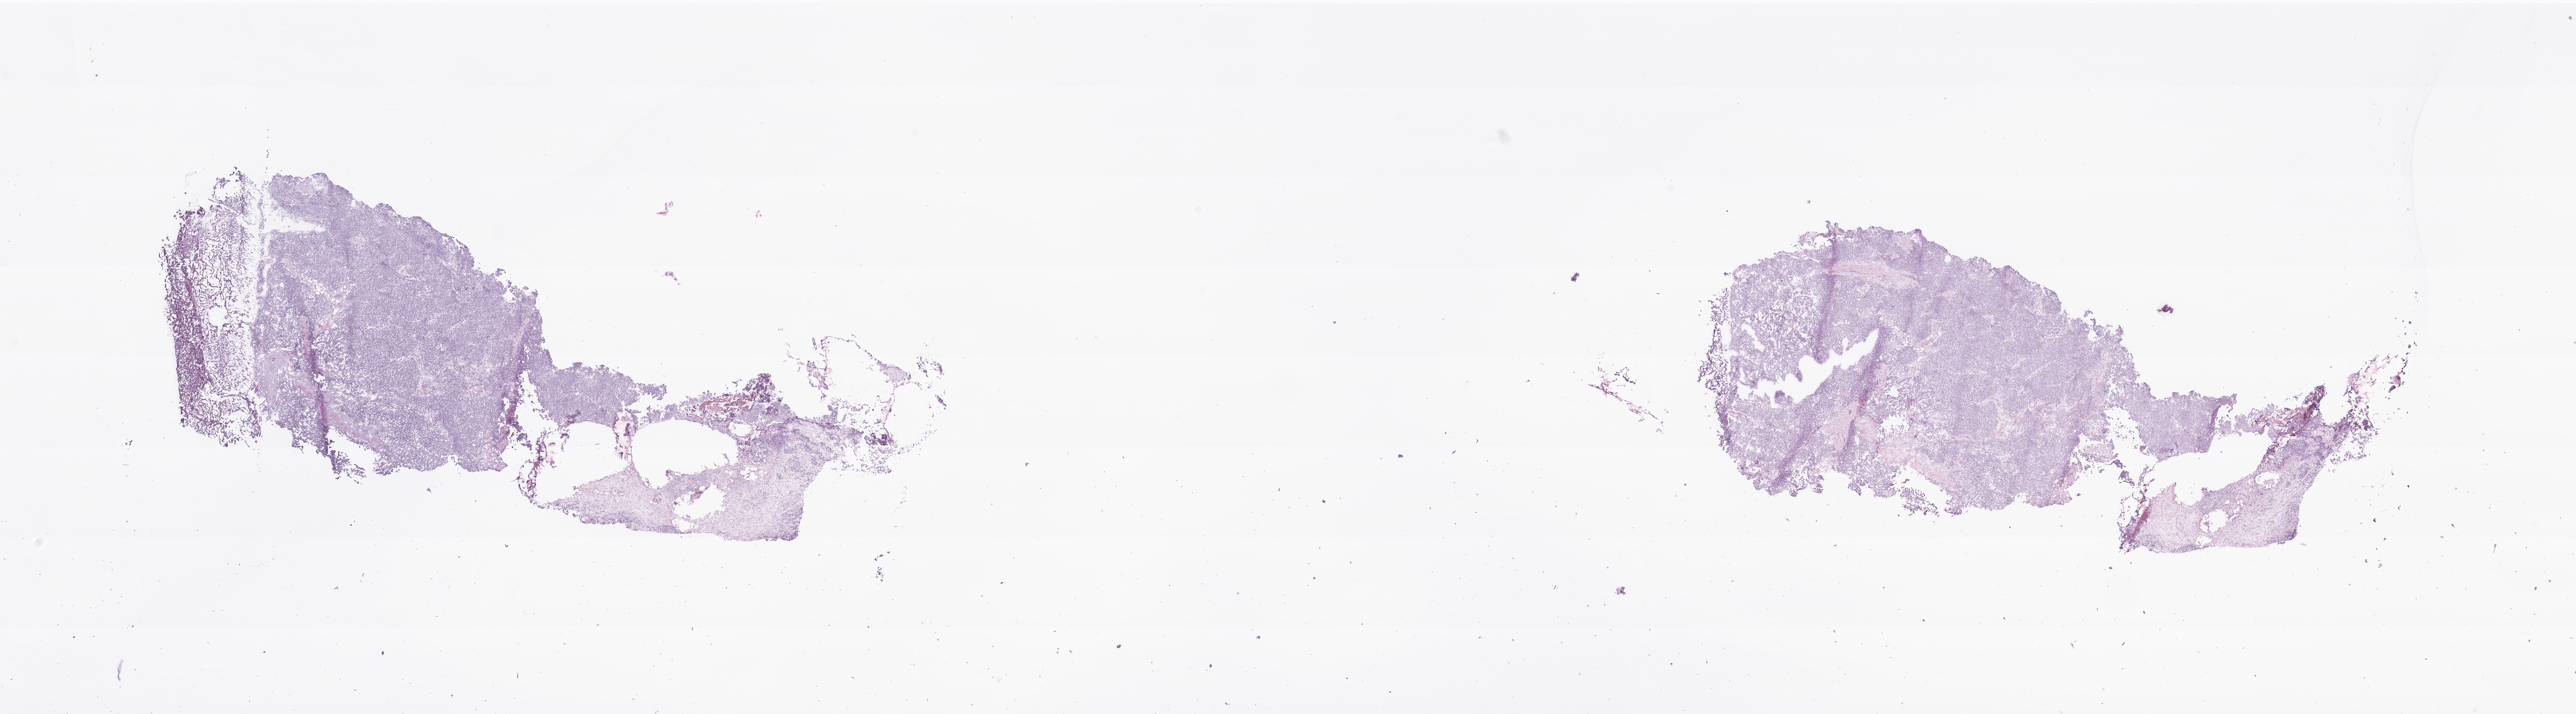
Hematoxylin and eosin (H&E) whole-slide image of tumor tissue from the abdomen, whole scanned area (about 30.4 x 8.4 mm) shown as a low-resolution overview. Frozen section. Patient: male, age 155 months (12 years 11 months).
* diagnosis: Sarcoma, NOS